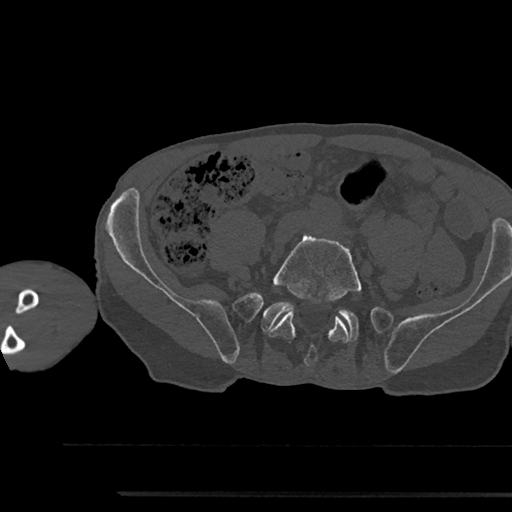
CT including the spine, one axial slice. Slice 333 of 797 in the series (ordered by position). 120 kVp. Bone window (W 1800 / L 400 HU). 0.5 mm slice thickness. 512 × 512 image matrix, field of view 367 × 367 mm. Male patient, age 79 years. From the clinical record (not read from this slice): primary cancer: prostate.
Structures marked on this image (semi-automatically segmented with operator editing):
- L5 vertebra: box from (x=268, y=234) to (x=362, y=366) px